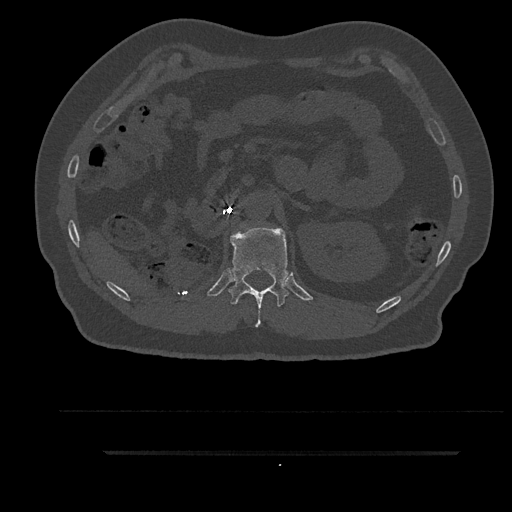
CT including the spine, one axial slice; bone window (W 1800 / L 400 HU); 0.5 mm slice thickness; 512 × 512 image matrix, field of view 432 × 432 mm. Patient: male, 63 years. From the clinical record (not read from this slice): primary cancer: renal; vertebrae with lytic lesions (as recorded): T8.
Annotated regions visible in this slice (semi-automatic segmentation, software-assisted and operator-edited):
- T12 vertebra: bounding box <229,225,289,327> (left, top, right, bottom; pixels)